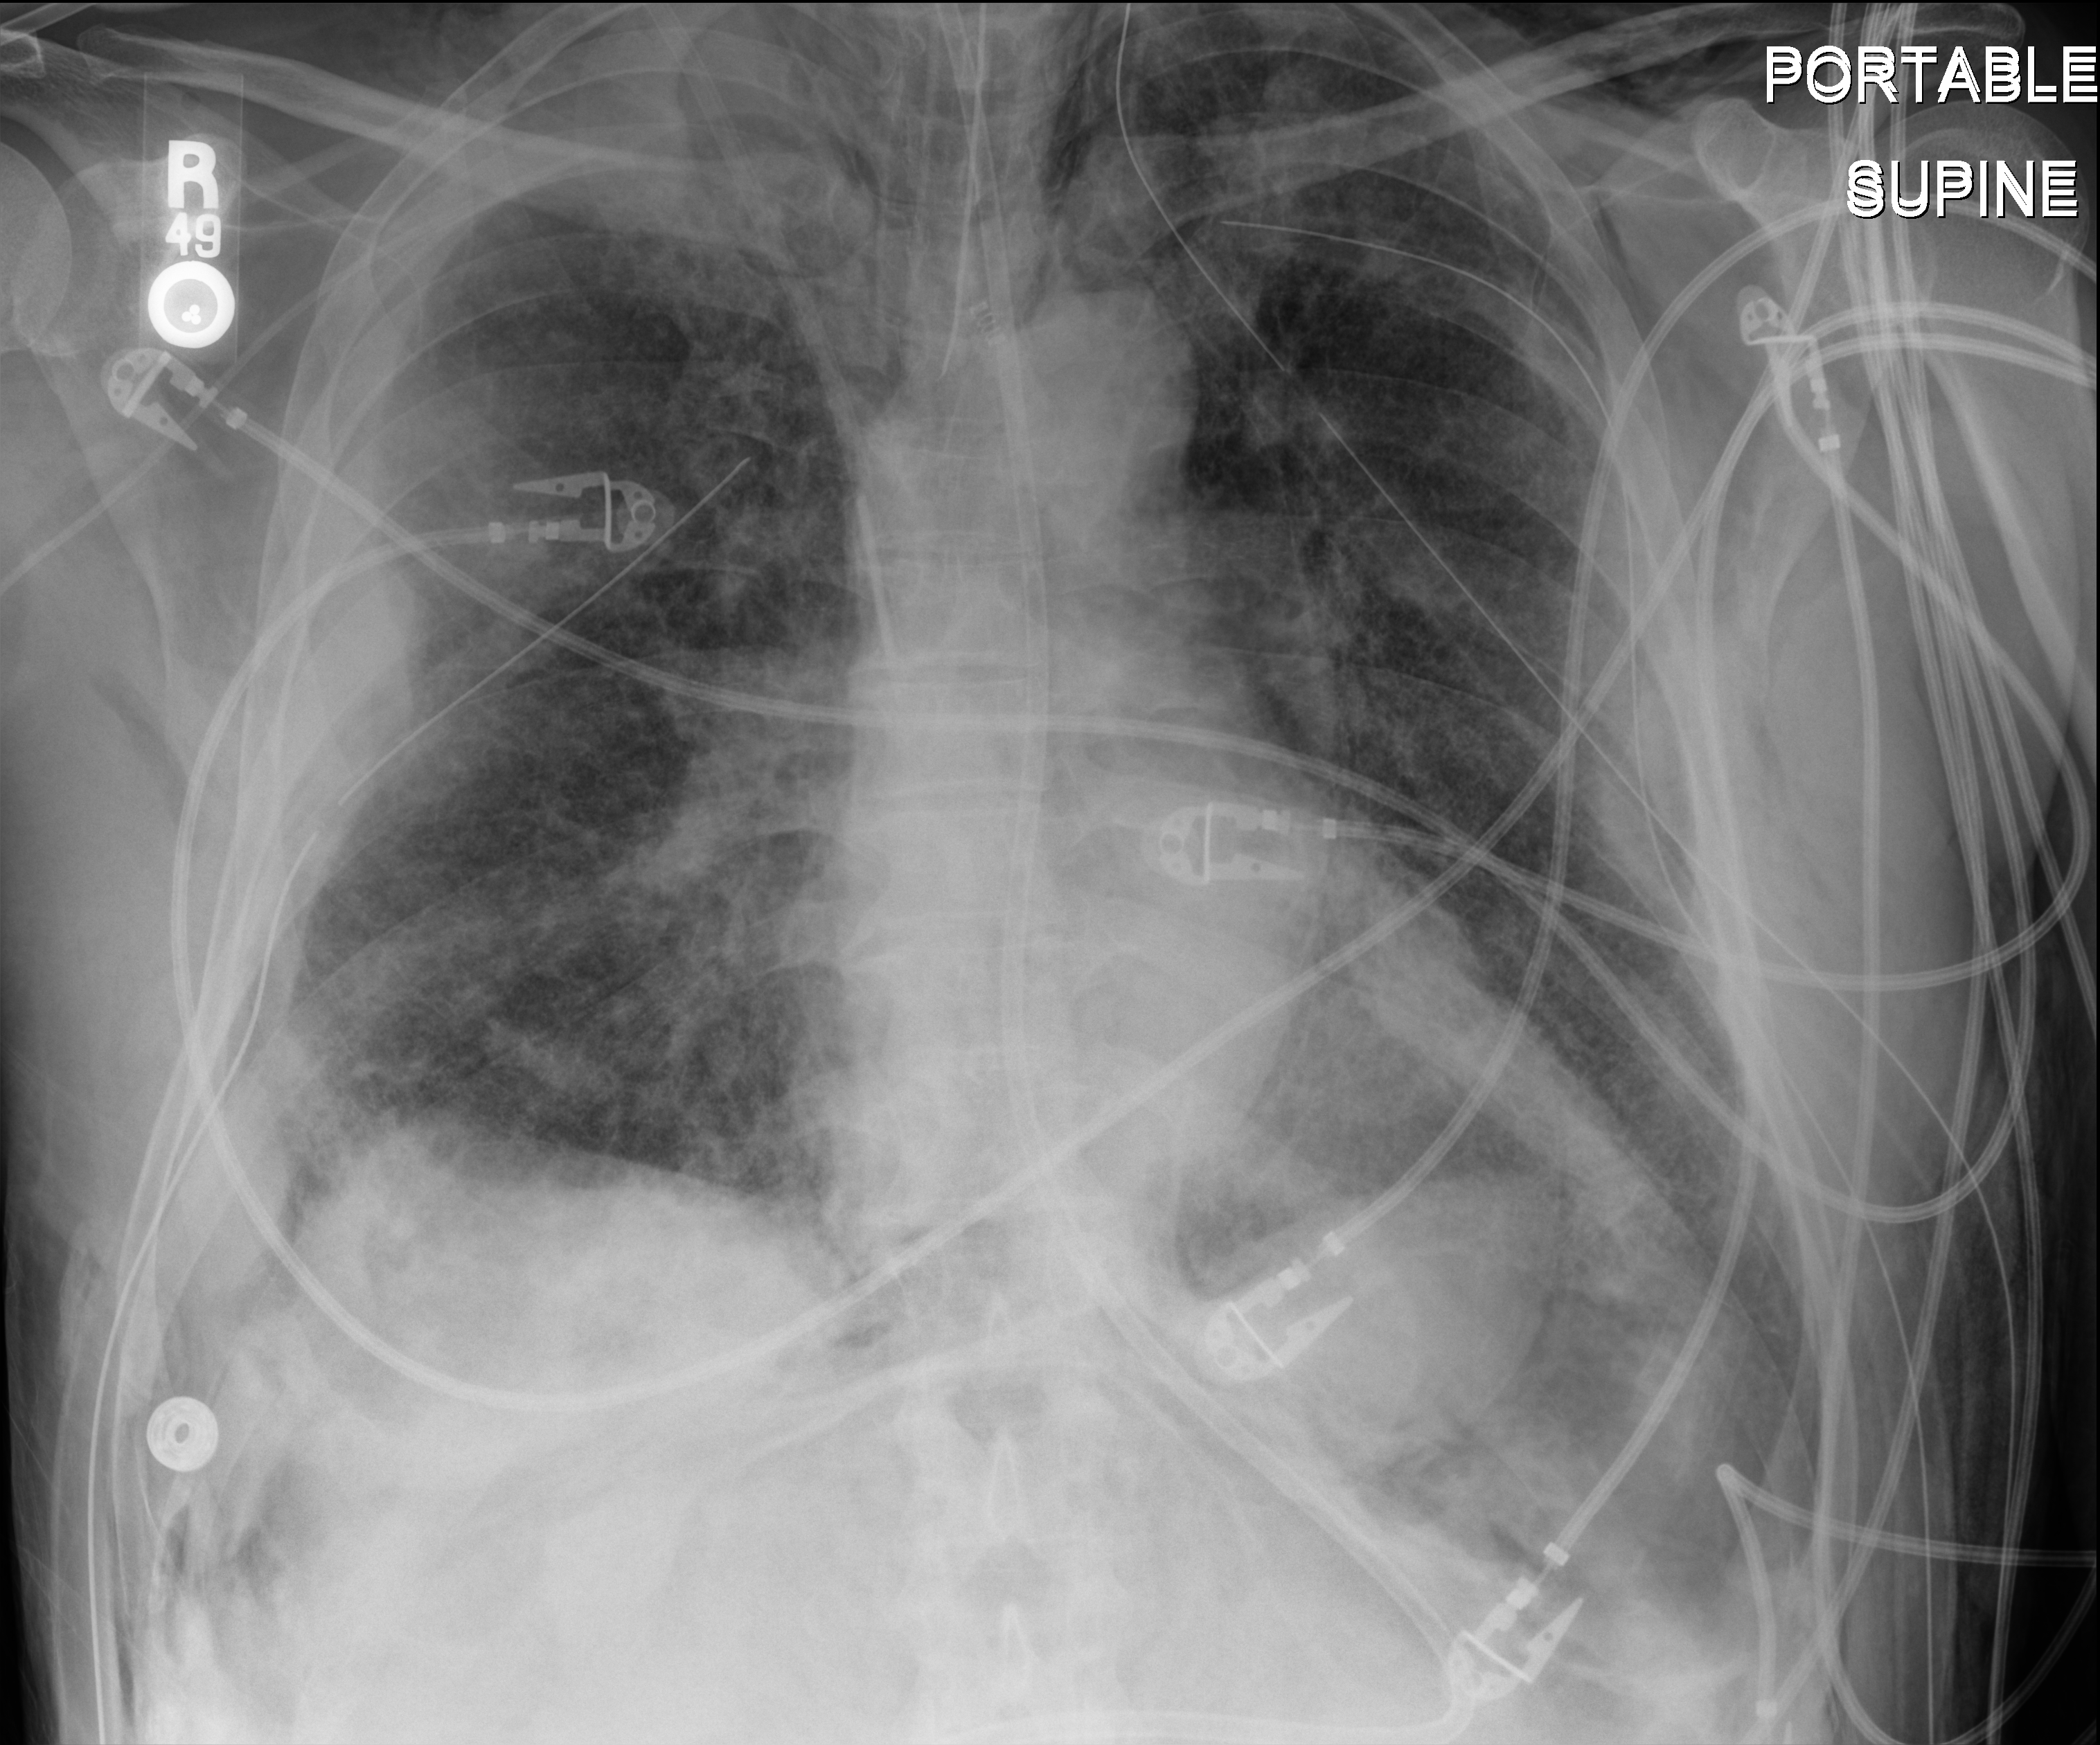
Chest X-ray (portable), anteroposterior (AP) projection. Patient hospitalised with COVID-19; male, aged 18–59 years.
From the hospital-stay record, not from the radiograph (when in the stay this image was taken is not recorded):
- COPD (admission record): no
- admitted to intensive care during this hospital stay: yes